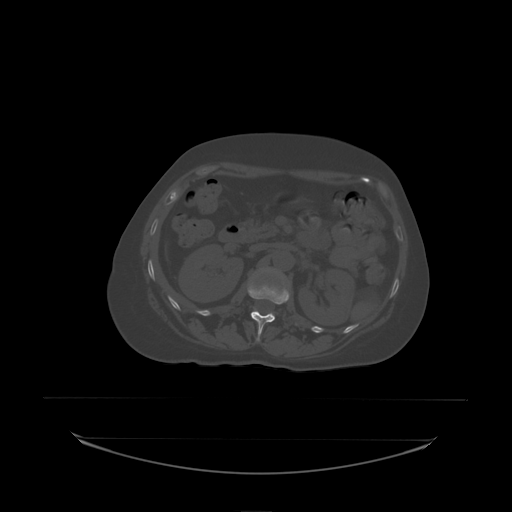
CT including the spine, one axial slice; slice 81 of 242 in the series (ordered by position); bone window (W 1800 / L 400 HU); 2.5 mm slice thickness; 512 × 512 image matrix, field of view 500 × 500 mm. Female patient, age 53 years. Case-level facts recorded for this patient, not image findings: primary cancer: lung; vertebrae with lytic lesions (as recorded): T7, L1.
Annotated regions visible in this slice (semi-automatic segmentation, software-assisted and operator-edited):
- L1 vertebra: bounding box (x1, y1, x2, y2) in pixels: (248, 286, 297, 338)
- L2 vertebra: (260, 269, 283, 278)